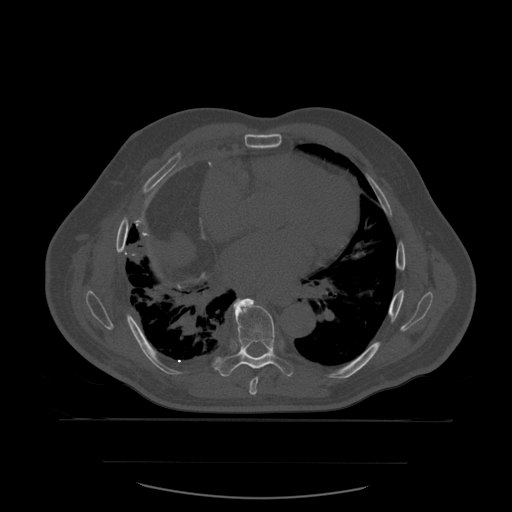
CT including the spine, one axial slice. Position 365 of 590 along the scan axis. Bone window (W 1800 / L 400 HU). 512 × 512 image matrix, field of view 479 × 479 mm. Patient age 71 years. From the clinical record (not read from this slice): primary cancer: lung; vertebrae with lytic lesions (as recorded): T1, T2, L5, S1.
Structures marked on this image (semi-automatically segmented with operator editing):
- T7 vertebra: bounding box (x1, y1, x2, y2) in pixels: (250, 377, 259, 396)
- T8 vertebra: (218, 299, 294, 377)